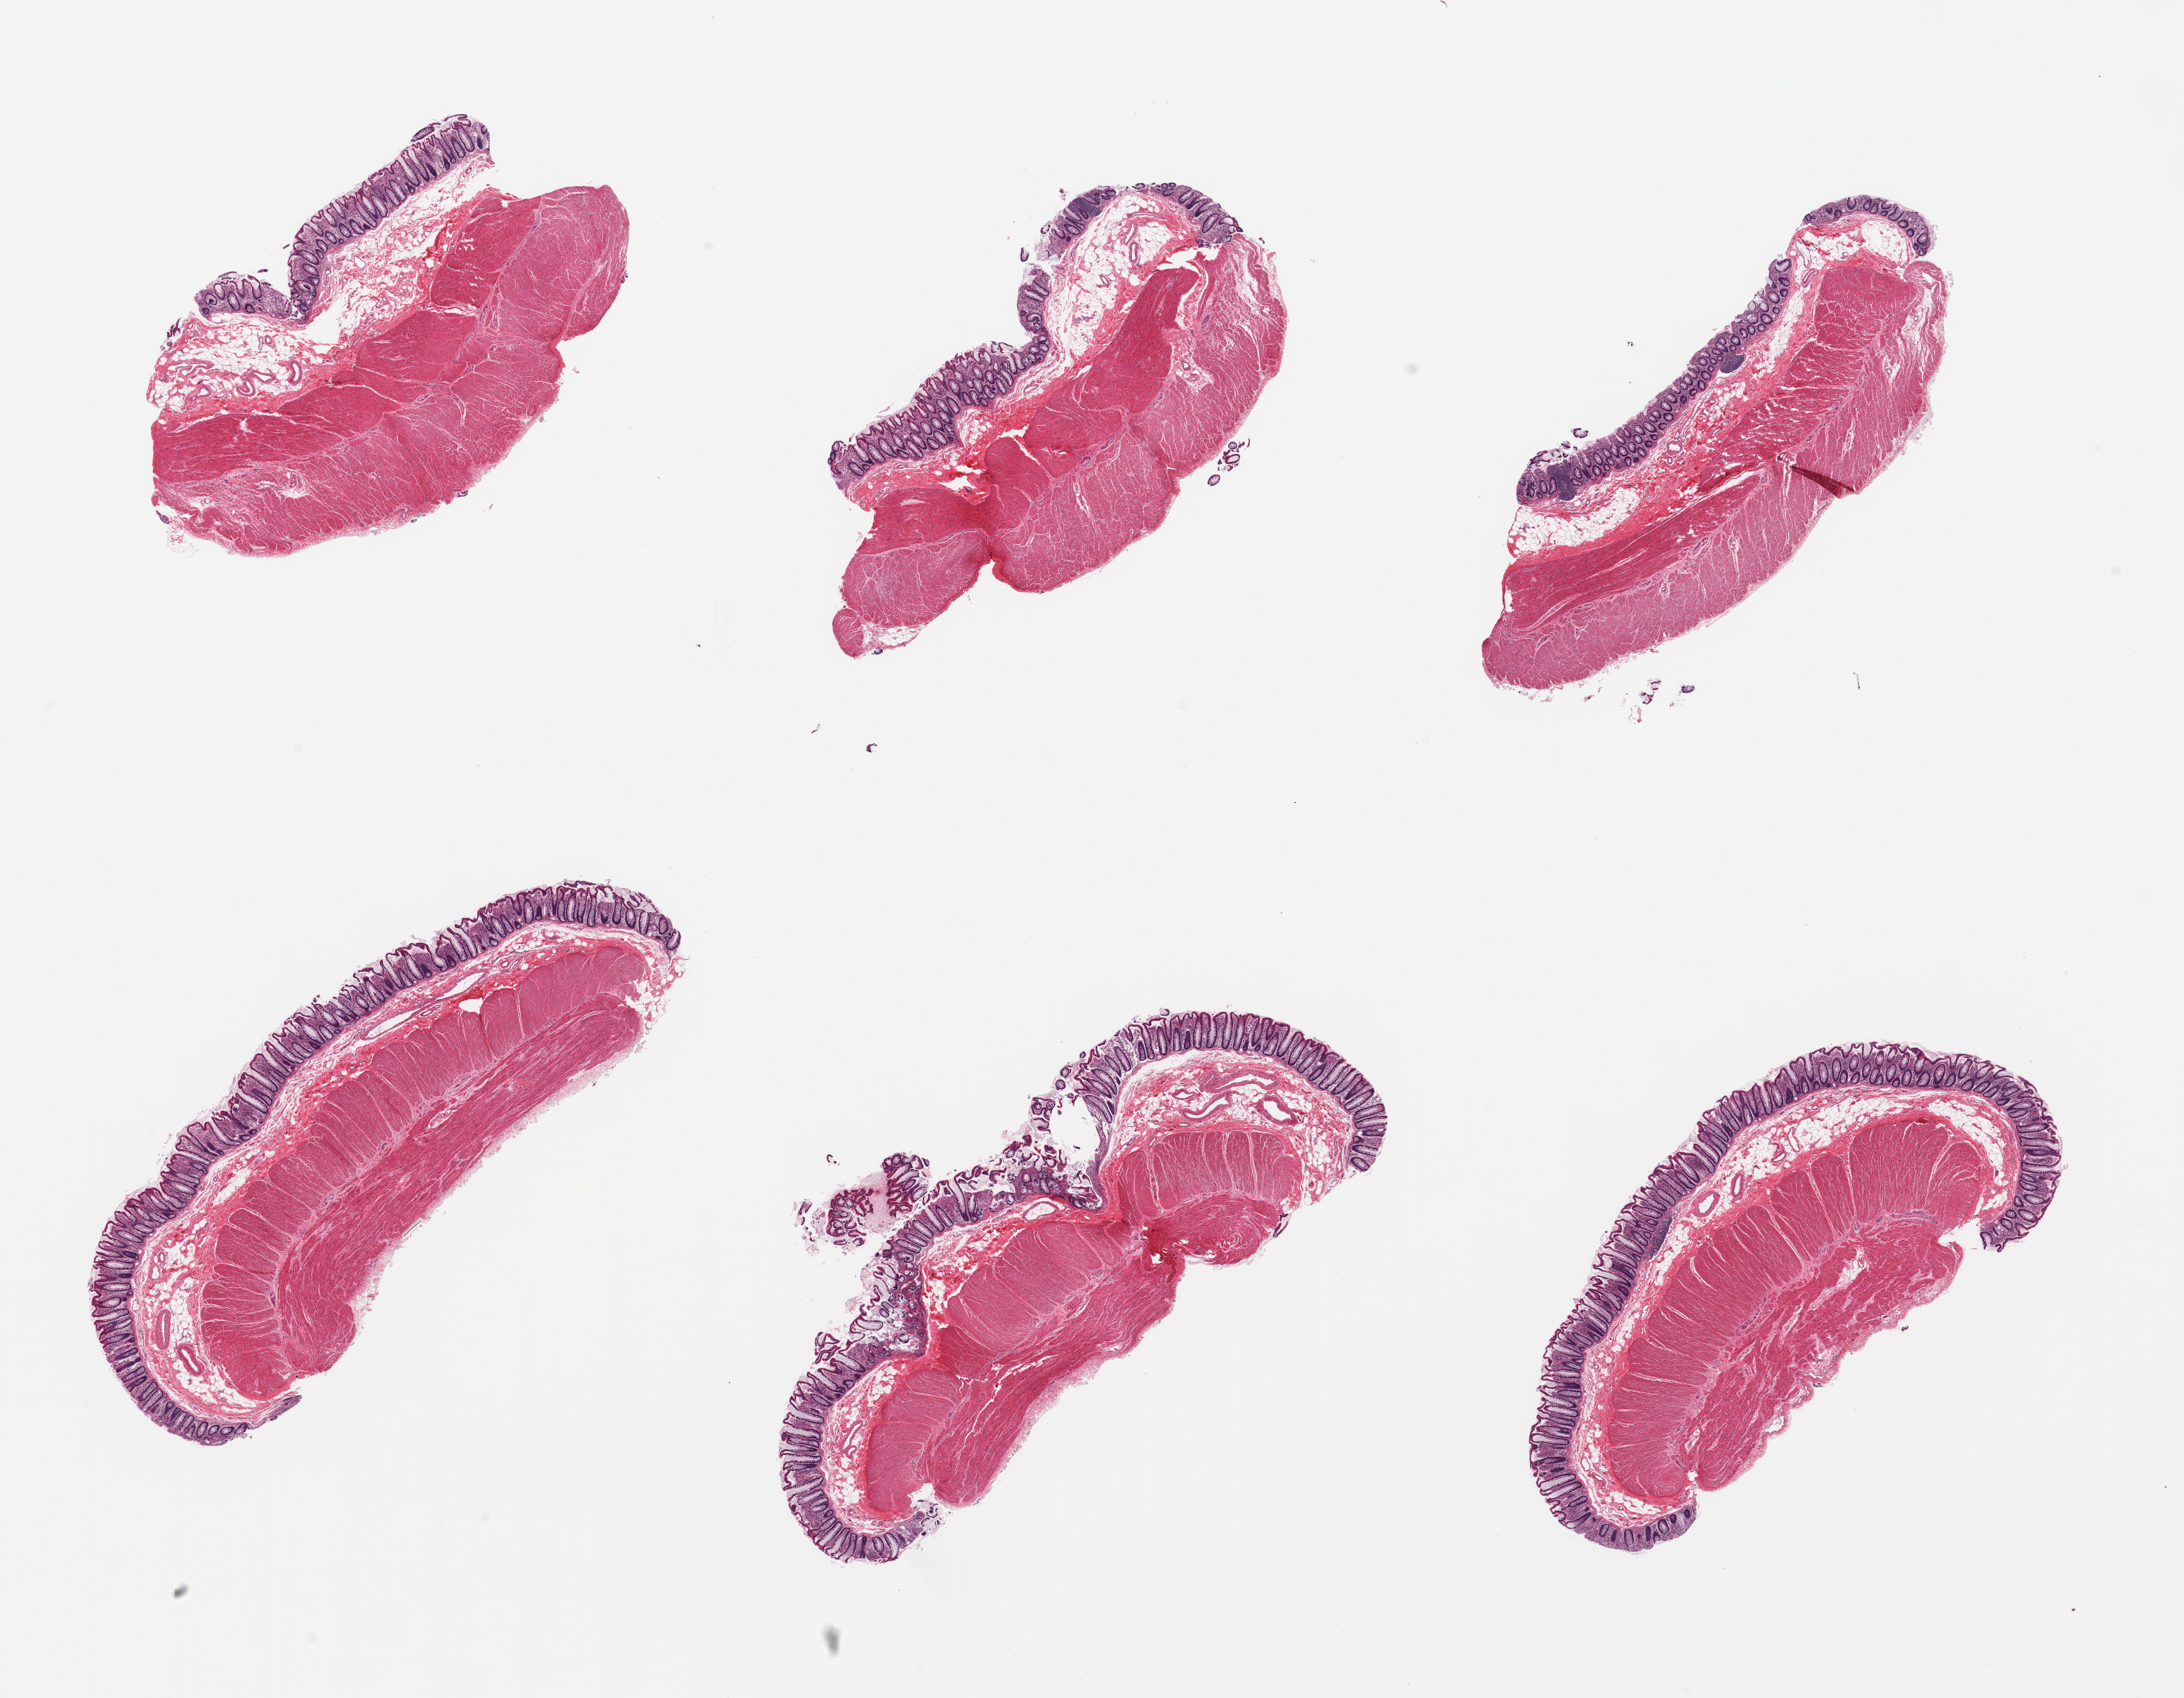
Digitized haematoxylin and eosin-stained section, a low-resolution overview of the entire scanned area, about 24.6 x 19.1 mm. PAXgene-fixed paraffin-embedded (PFPE) section. Section of transverse colon (target tissue). Tissue donor sample. Female donor.
- pathologist's review note for this sample: 6 pieces; full thickness; well preserved; well dissected